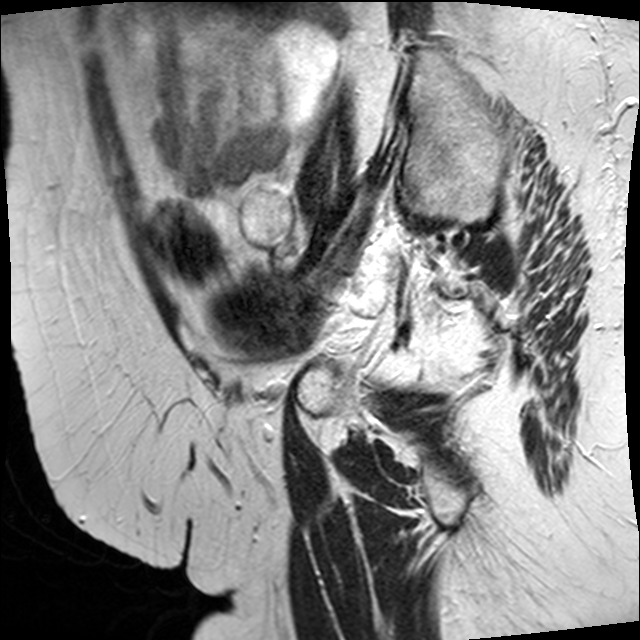
Pelvic MRI for cervical cancer, one sagittal slice; T2-weighted; 1.5 T; TE 89 ms, TR 4610 ms; 4 mm slice thickness; 640 × 640 image matrix, field of view 260 × 260 mm. Patient: female, 50 years.
Outlined on this slice (expert manual segmentation):
- uterus and cervix: bounding box (x1, y1, x2, y2) in pixels: (209, 261, 334, 366)